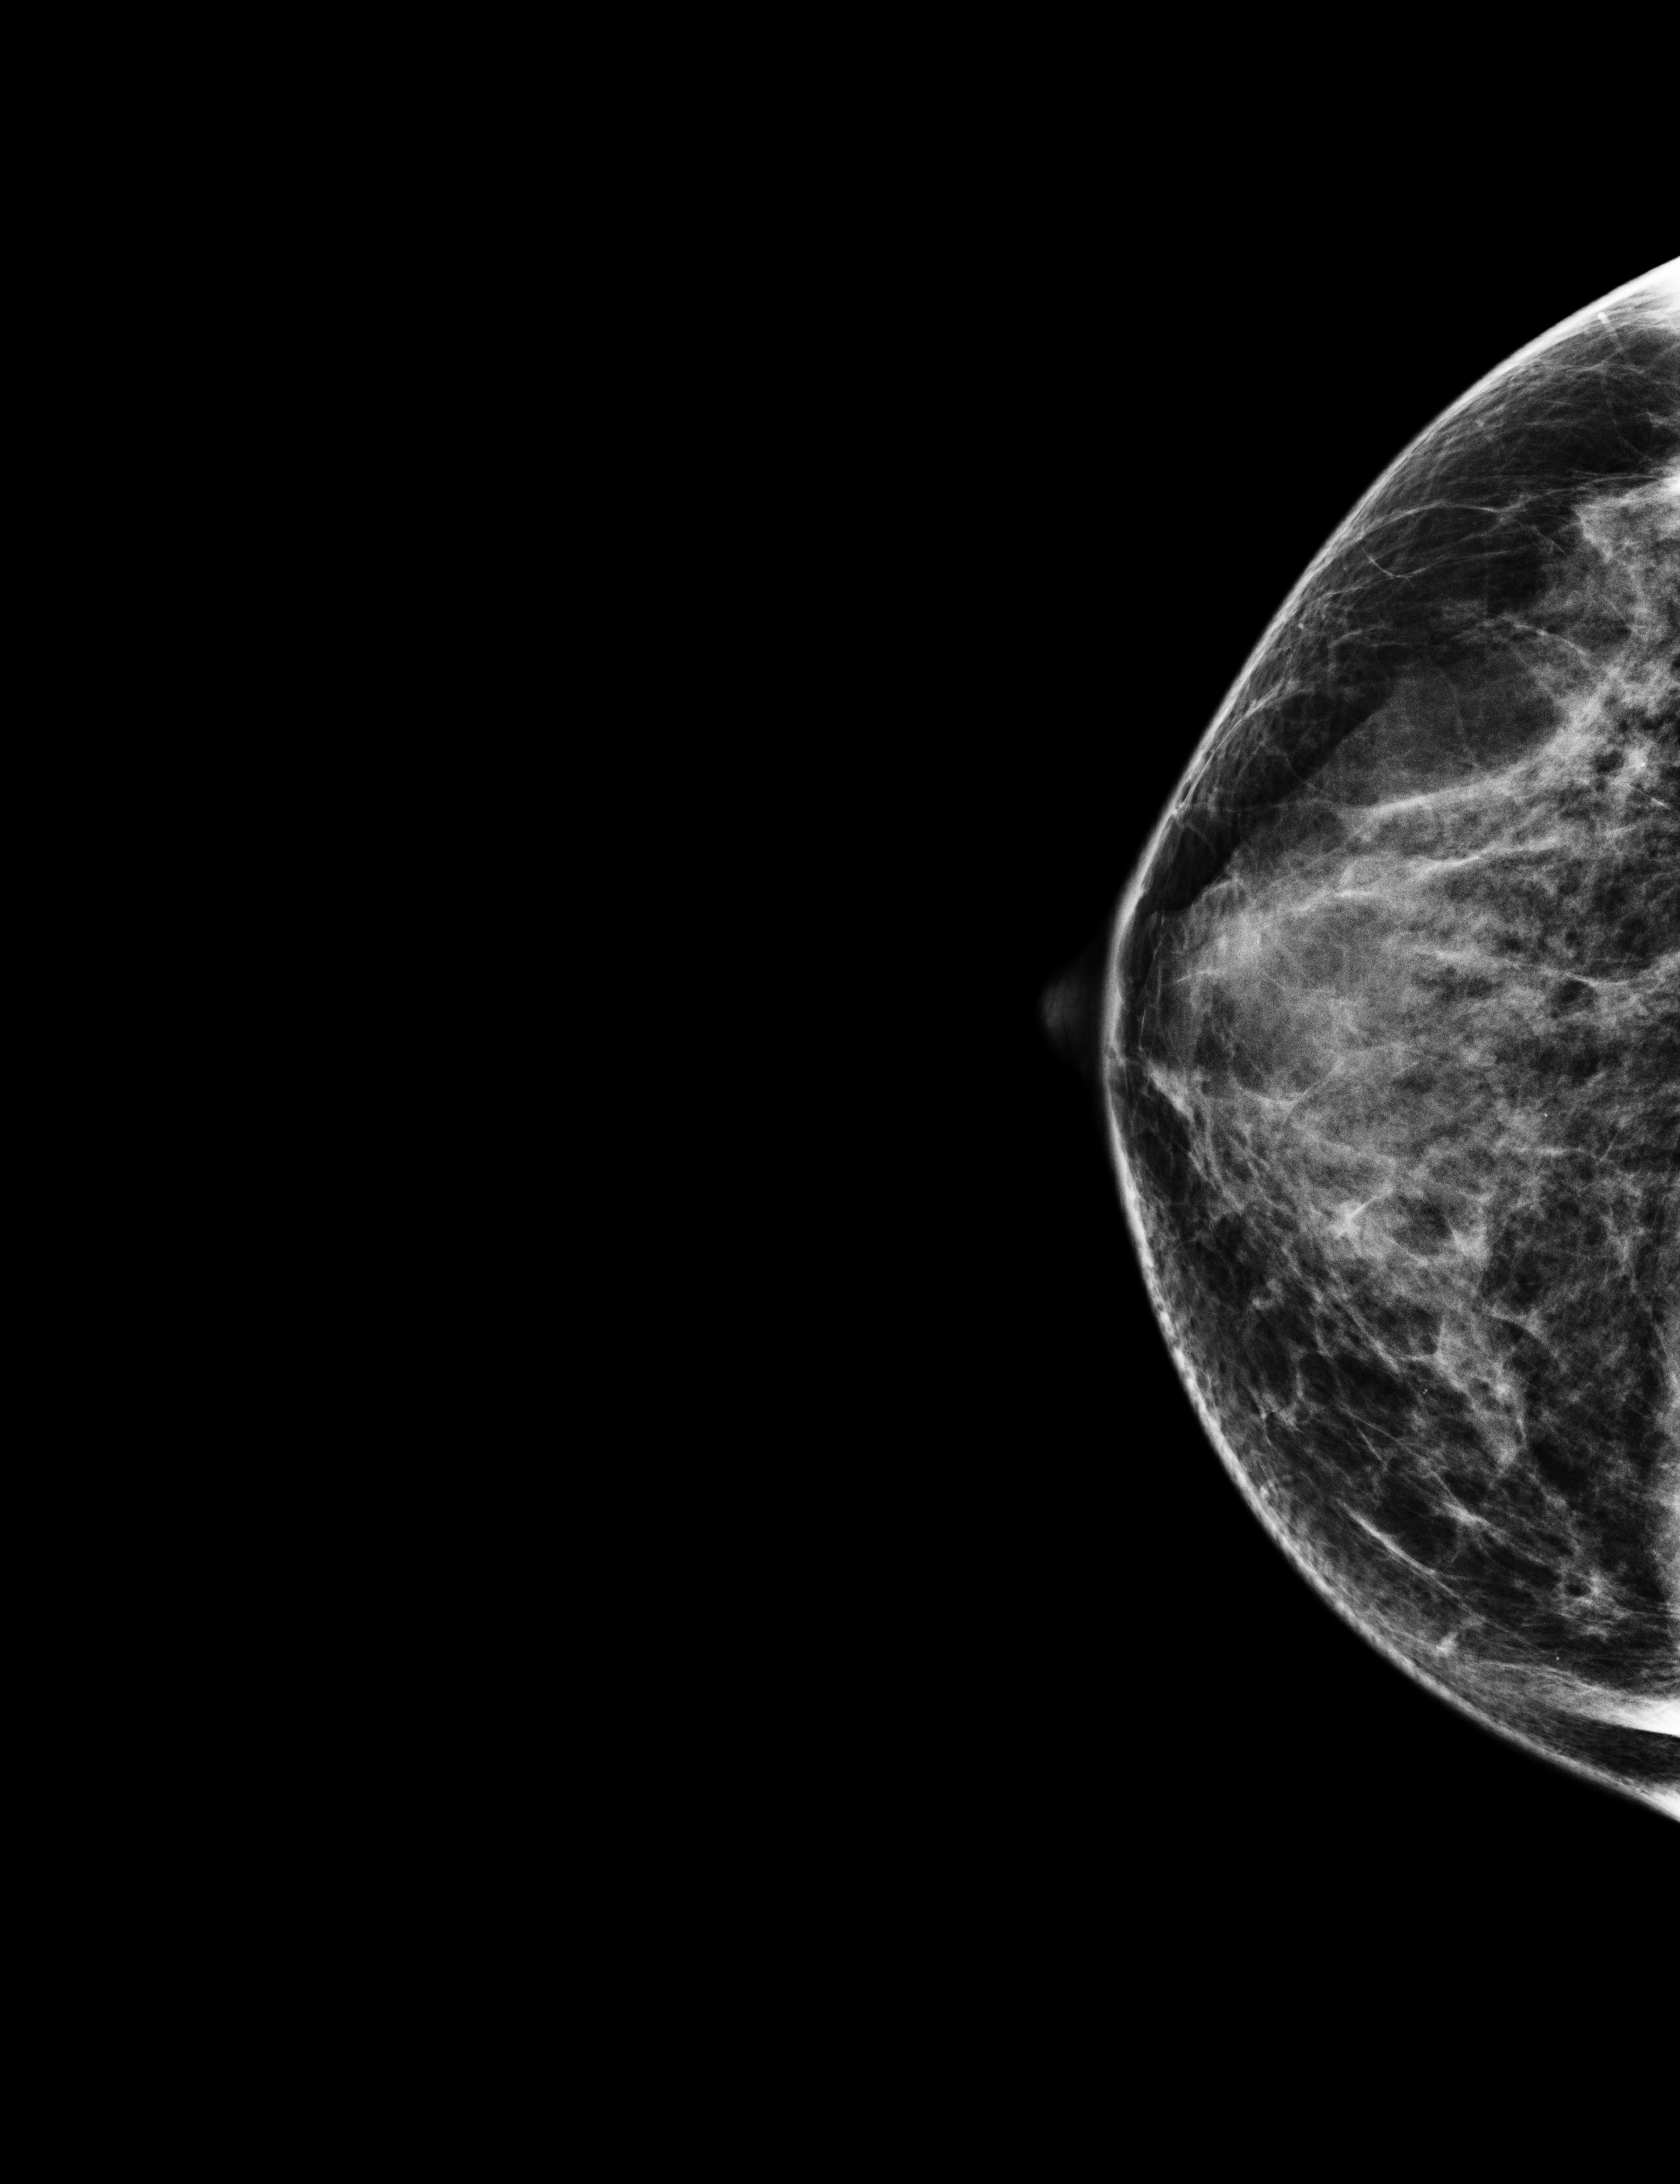
Annual screening mammography examination. Female patient, age 55 years.
Image type: full-field digital mammogram. Breast: right. Projection: craniocaudal (CC) view.